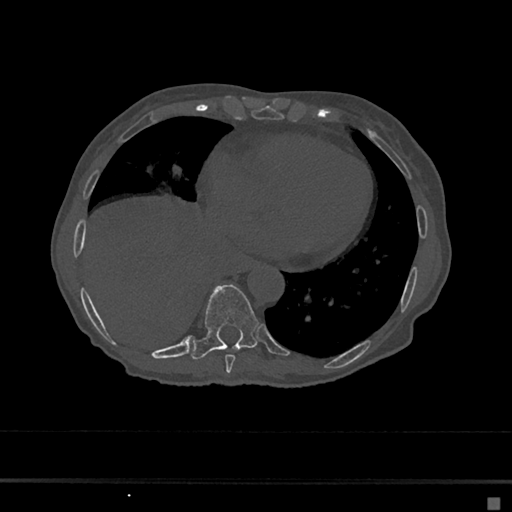
CT including the spine, one axial slice. Reconstruction kernel Br40s/3. Bone window (W 1800 / L 400 HU). 0.5 mm slice thickness. 512 × 512 image matrix, field of view 360 × 360 mm. Female patient, age 68 years. From the clinical record (not read from this slice): primary cancer: renal.
Structures marked on this image (semi-automatic segmentation, software-assisted and operator-edited):
- T8 vertebra: bounding box (x1, y1, x2, y2) in pixels: (225, 355, 236, 373)
- T9 vertebra: (191, 284, 259, 359)